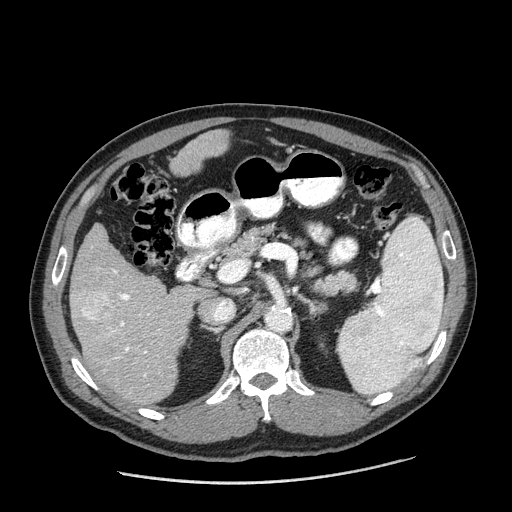
Contrast-enhanced abdominal CT (liver protocol), one axial slice; reconstruction kernel STANDARD; 120 kVp; one of 2 acquisitions stored at this slice position; soft-tissue window (W 400 / L 40 HU); 512 × 512 image matrix, field of view 400 × 400 mm. Case-level facts recorded for this patient, not image findings: diagnosis: hepatocellular carcinoma (patient treated with transarterial chemoembolisation; whether this scan precedes or follows treatment is not stated here); TNM stage (as recorded): Stage-II; Child-Pugh class: A; tumour differentiation: moderately differentiated; tumour nodularity: multinodular.
Annotated regions visible in this slice (semi-automatically segmented with operator editing):
- liver parenchyma outside the tumour (the mass and vessels are separate outlines, so this box may not span the whole liver): bounding box [x1, y1, x2, y2] px = [70, 130, 228, 404]
- mass: [79, 289, 111, 320]
- liver vessels: [108, 269, 149, 377]